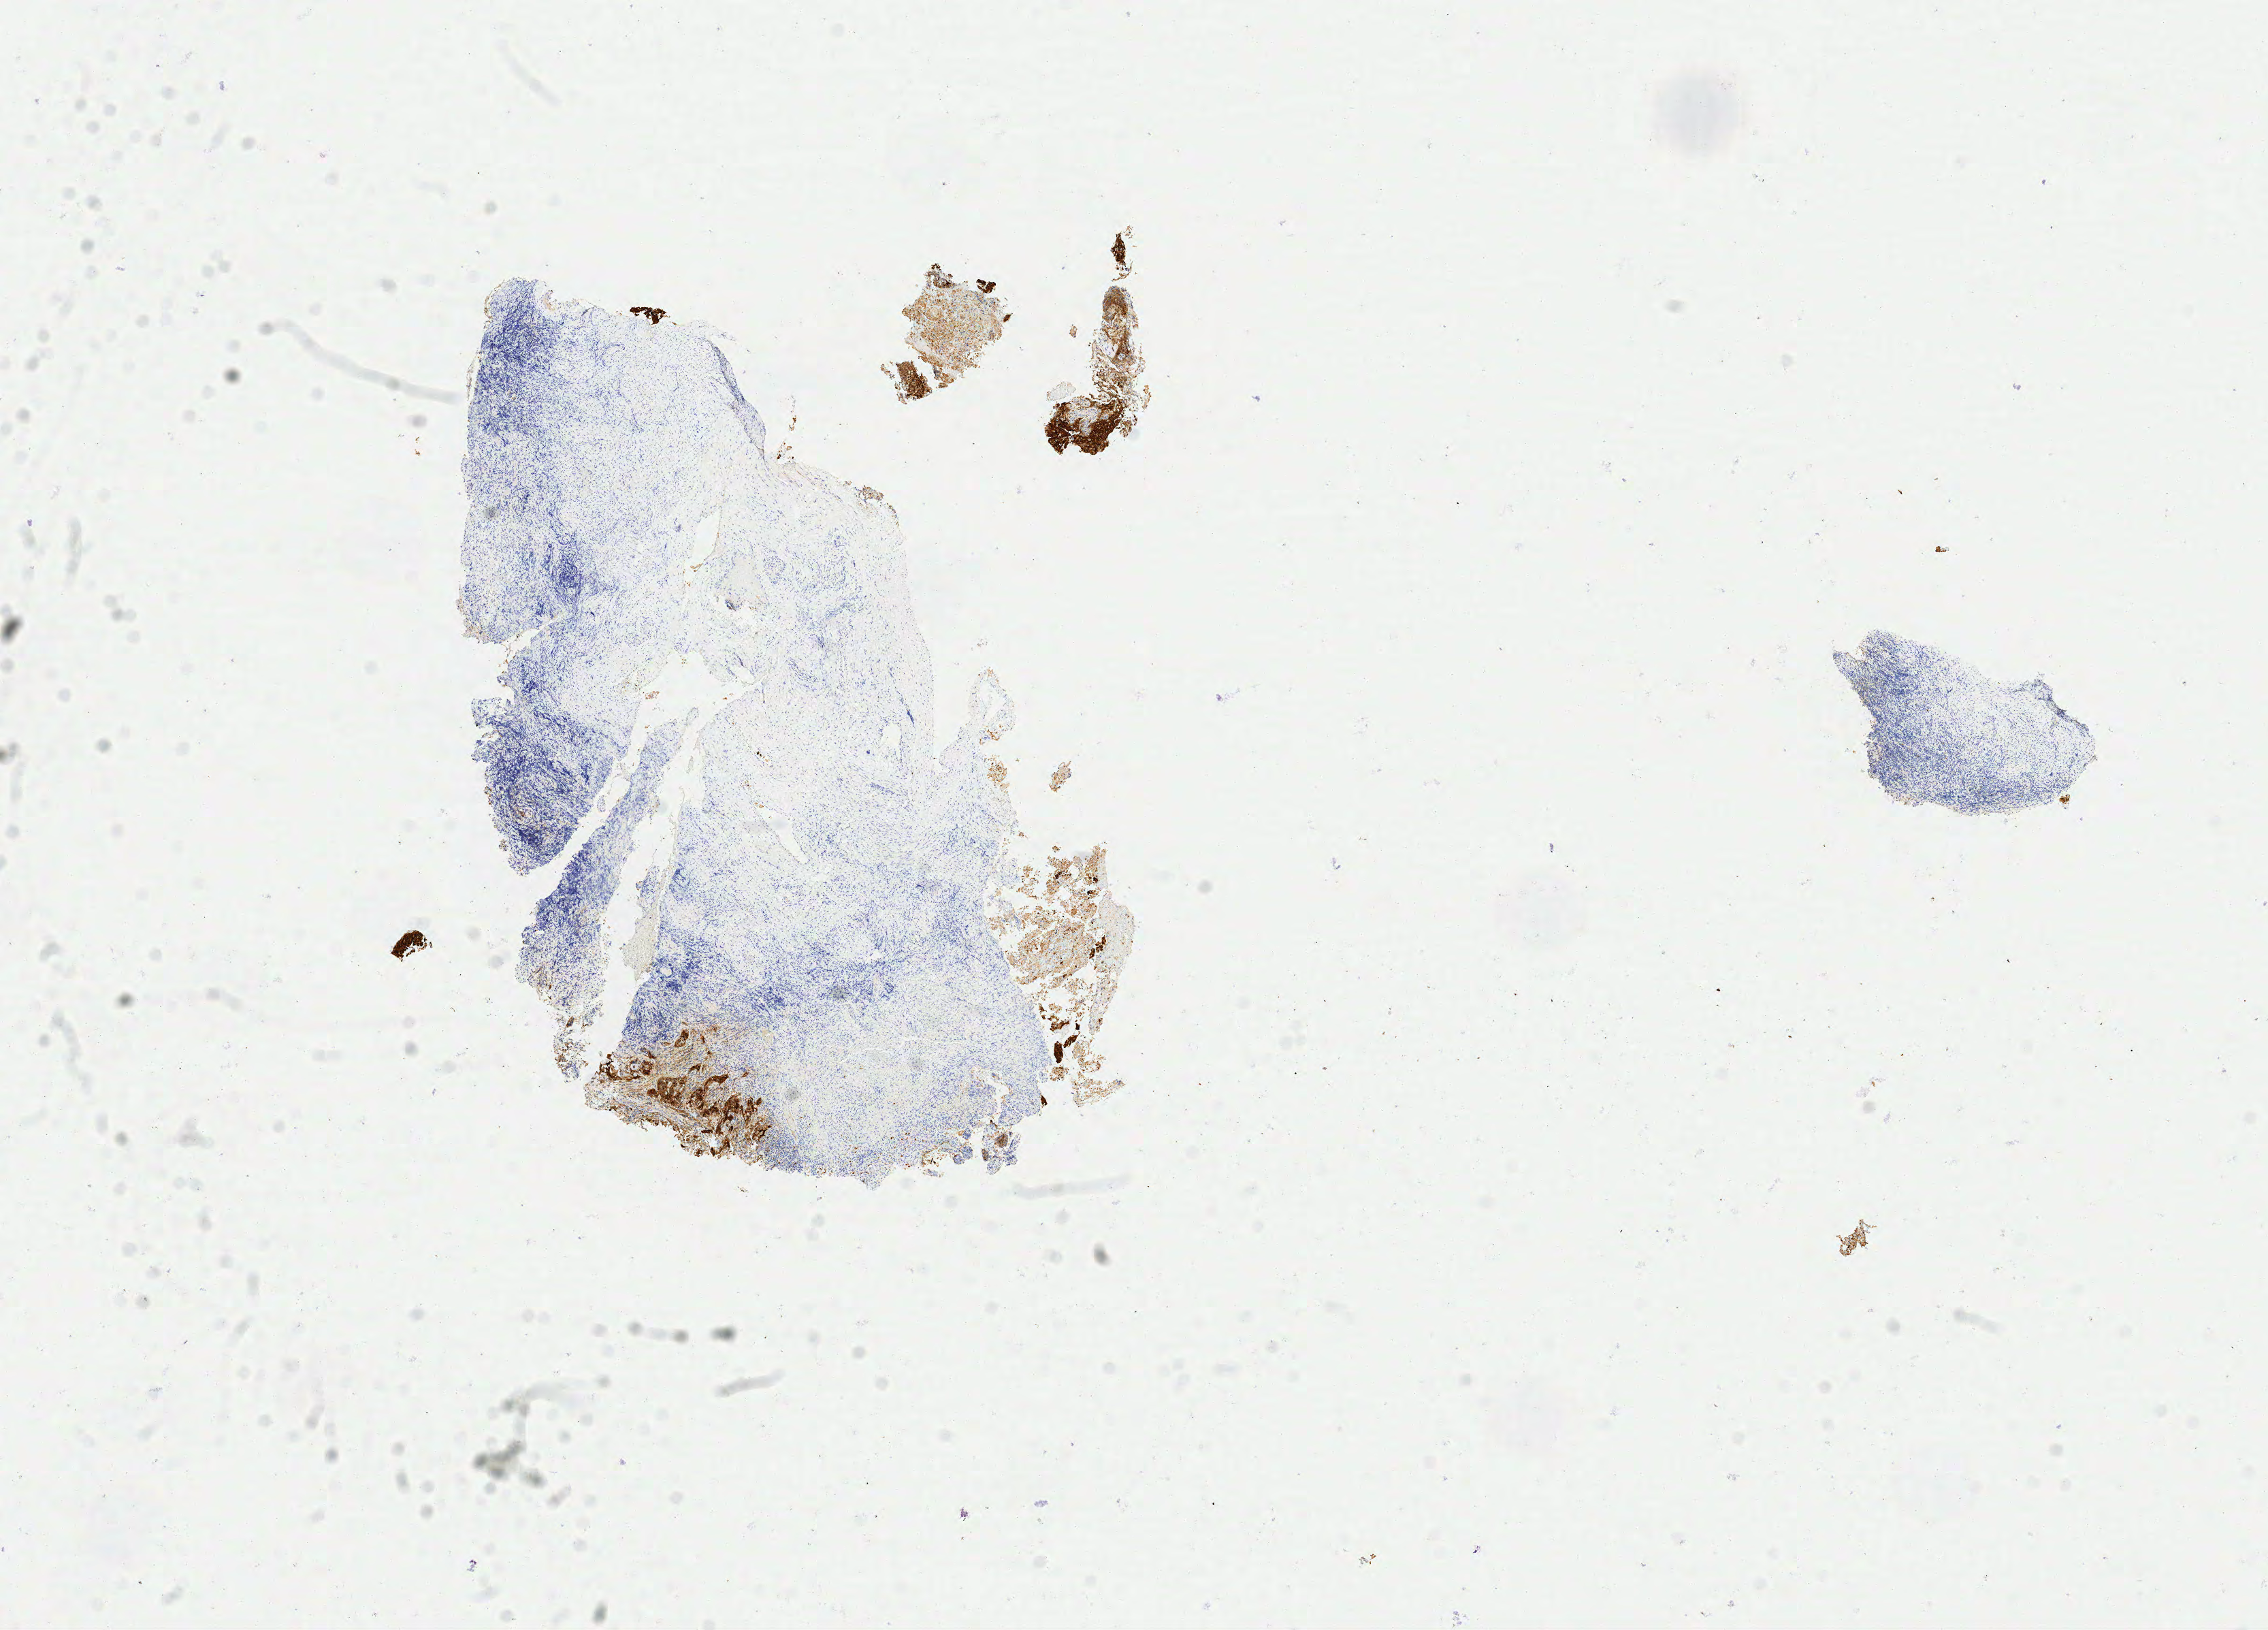
Immunohistochemistry (IHC) whole-slide image stained for p16 (p16INK4a) — low-resolution overview of the scanned area, about 13.3 x 9.5 mm, tumor tissue, anatomic site: cervix. Patient female; age 39 years.
Diagnosis: Squamous cell carcinoma, keratinizing, NOS.